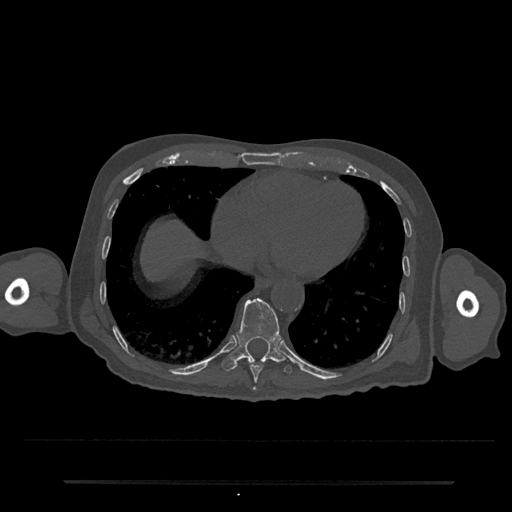
CT including the spine, one axial slice. Slice 331 of 797 in the series (ordered by position). 120 kVp. Bone window (W 1800 / L 400 HU). 0.5 mm slice thickness. 512 × 512 image matrix, field of view 427 × 427 mm. Patient: male, 74 years. From the clinical record (not read from this slice): primary cancer: prostate.
Annotated regions visible in this slice (semi-automatically segmented with operator editing):
- T10 vertebra: box from (x=222, y=298) to (x=292, y=374) px
- T9 vertebra: (x=250, y=361)–(x=263, y=390)